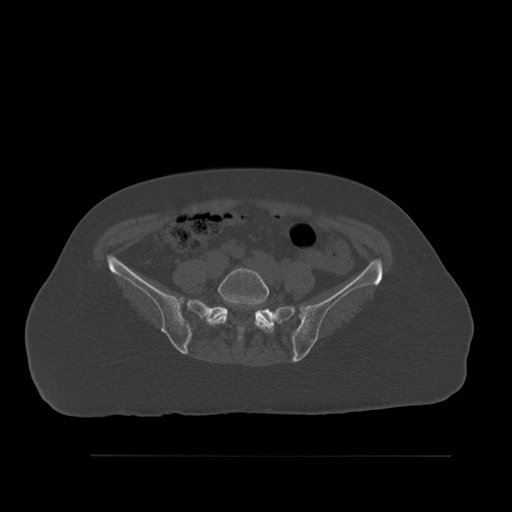
CT including the spine, one axial slice; position 182 of 527 along the scan axis; bone window (W 1800 / L 400 HU); 512 × 512 image matrix. Patient: female, 73 years. Case-level facts recorded for this patient, not image findings: primary cancer: breast; vertebrae with lytic lesions (as recorded): L2.
Annotated regions visible in this slice (semi-automatically segmented with operator editing):
- L5 vertebra: box from (x=207, y=268) to (x=274, y=333) px